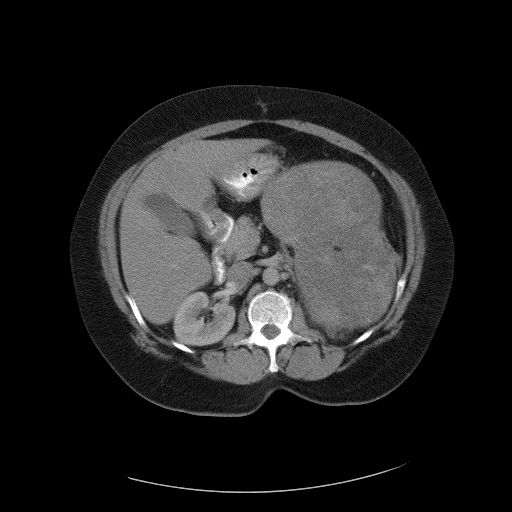
Contrast-enhanced abdominal CT, one axial slice. Slice 63 of 90 in the series (ordered by position). Reconstruction kernel FC01. 120 kVp. Soft-tissue window (W 400 / L 40 HU). 5 mm slice thickness. 512 × 512 image matrix, field of view 480 × 480 mm. Patient: female, 55 years. From the clinical record (not read from this slice): diagnosis: adrenocortical carcinoma; tumour side: left adrenal; tumour size at pathology: 22 cm; Ki-67 index: 10 %; stage (as recorded): 3.
Annotated regions visible in this slice (semi-automatically segmented with operator editing):
- mass: bounding box <265,162,392,335> (left, top, right, bottom; pixels)